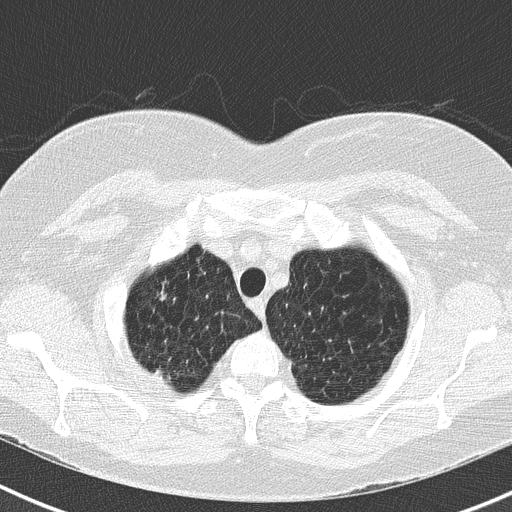
Axial slice from a low-dose chest CT screening exam. Second screening round (one year after baseline). Lung window (W 1500 / L -600 HU). 2 mm slice thickness. 120 kVp. Slice 29 of 183 in the series. Female, age 73 years at enrolment. Former smoker at enrolment.
• Expert reader's lesion annotation, bounding box [x1, y1, x2, y2] px = [143, 274, 187, 313].
• The screening reader recorded 2 non-calcified nodules or masses ≥4 mm on this exam (right upper lobe, right upper lobe); which of them this box marks is not recorded.
• Official screen result: positive, no significant change: stable abnormalities potentially related to lung cancer, unchanged since the prior screening exam.
• Lung cancer was diagnosed 250 days after this screen: adenocarcinoma, NOS, right upper lobe, moderately differentiated (G2), stage IB (AJCC 6th edition), 15 mm at pathology.